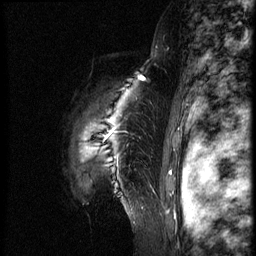
Breast MRI (dynamic contrast-enhanced), one sagittal slice; position 57 of 66 along the scan axis; dynamic contrast-enhanced series, image 2 of 3 at this slice position (ordered by acquisition); 1.5 T; TE 4.2 ms, TR 8.9 ms; 2.5 mm slice thickness; 256 × 256 image matrix. Patient: female, 39 years. From the clinical record (not read from this slice): setting: breast cancer imaged before/during neoadjuvant chemotherapy; receptor status: HER2-positive.
Structures marked on this image (semi-automatic segmentation, software-assisted and operator-edited):
- analysis volume of interest (the breast-tissue region the enhancement analysis was run in; not a lesion): bounding box <62,75,162,218> (left, top, right, bottom; pixels)
- tumour enhancement mask (voxels above the 140 % enhancement threshold inside the analysis volume of interest): <142,78,145,81>